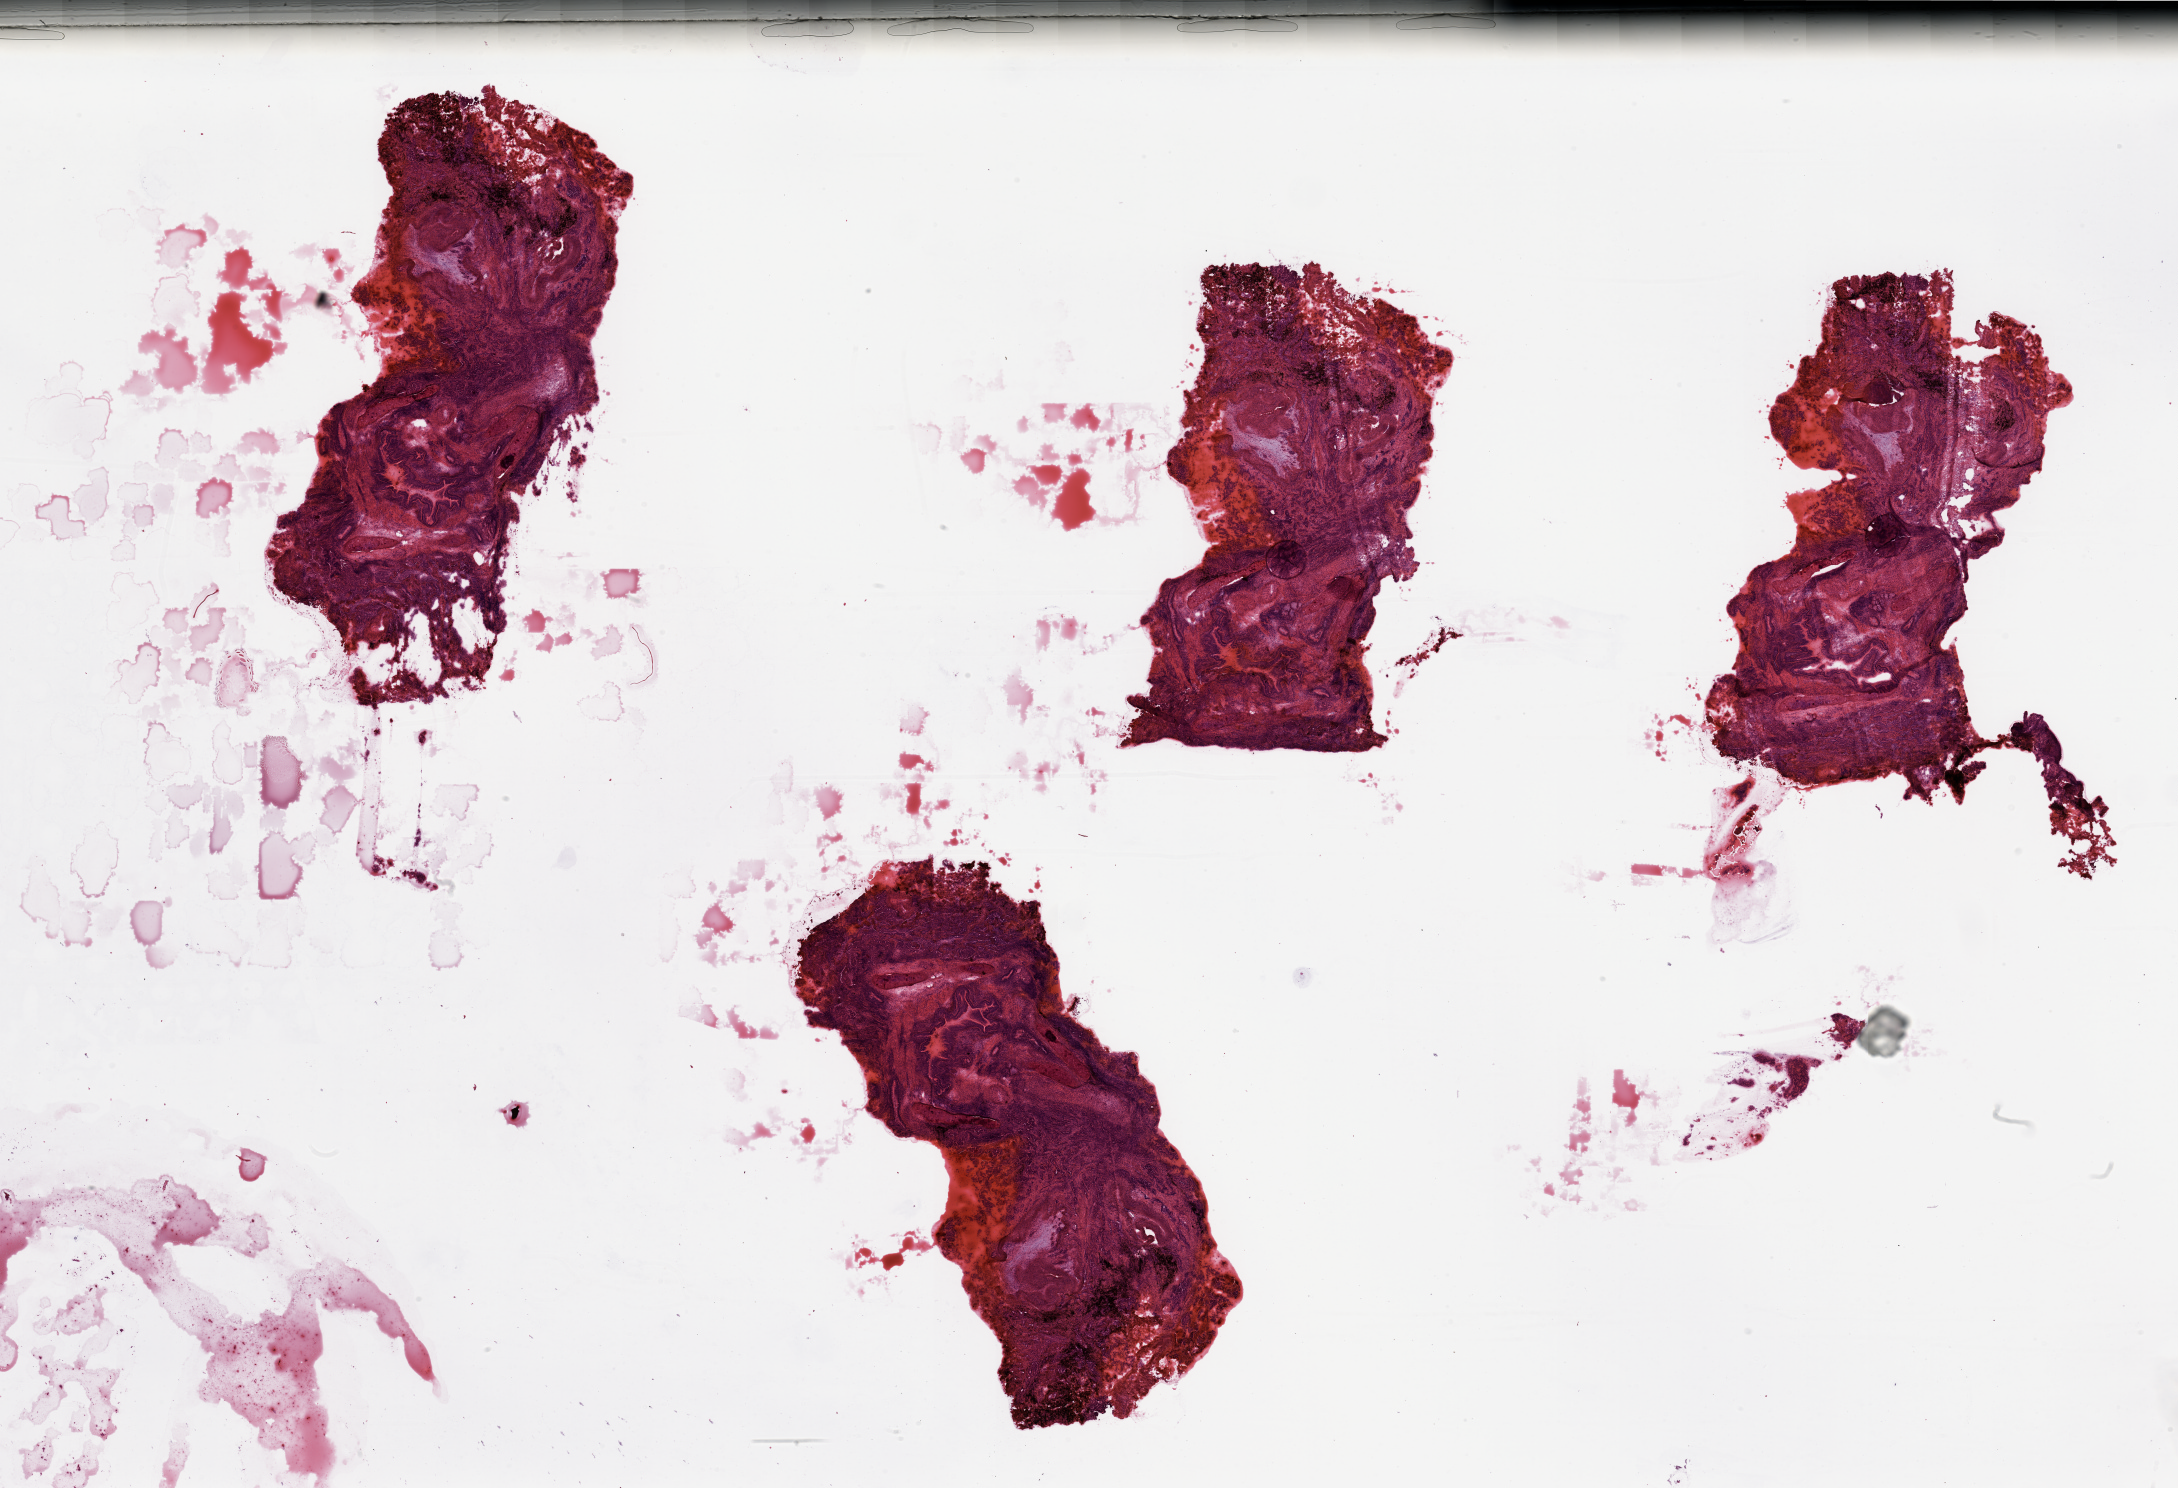
Digitized Hematoxylin and eosin (H&E) stained tissue section (whole slide), a low-resolution overview of the entire scanned area, about 34.5 x 23.5 mm (slide scanned at 20x), lung, tumour tissue. Male, 73 y/o. Histologic grade: GX (grade cannot be assessed).
AJCC pathologic stage: IB. Primary tumour site (as recorded): right upper lobe. Histologic diagnosis: Adenocarcinoma, NOS.